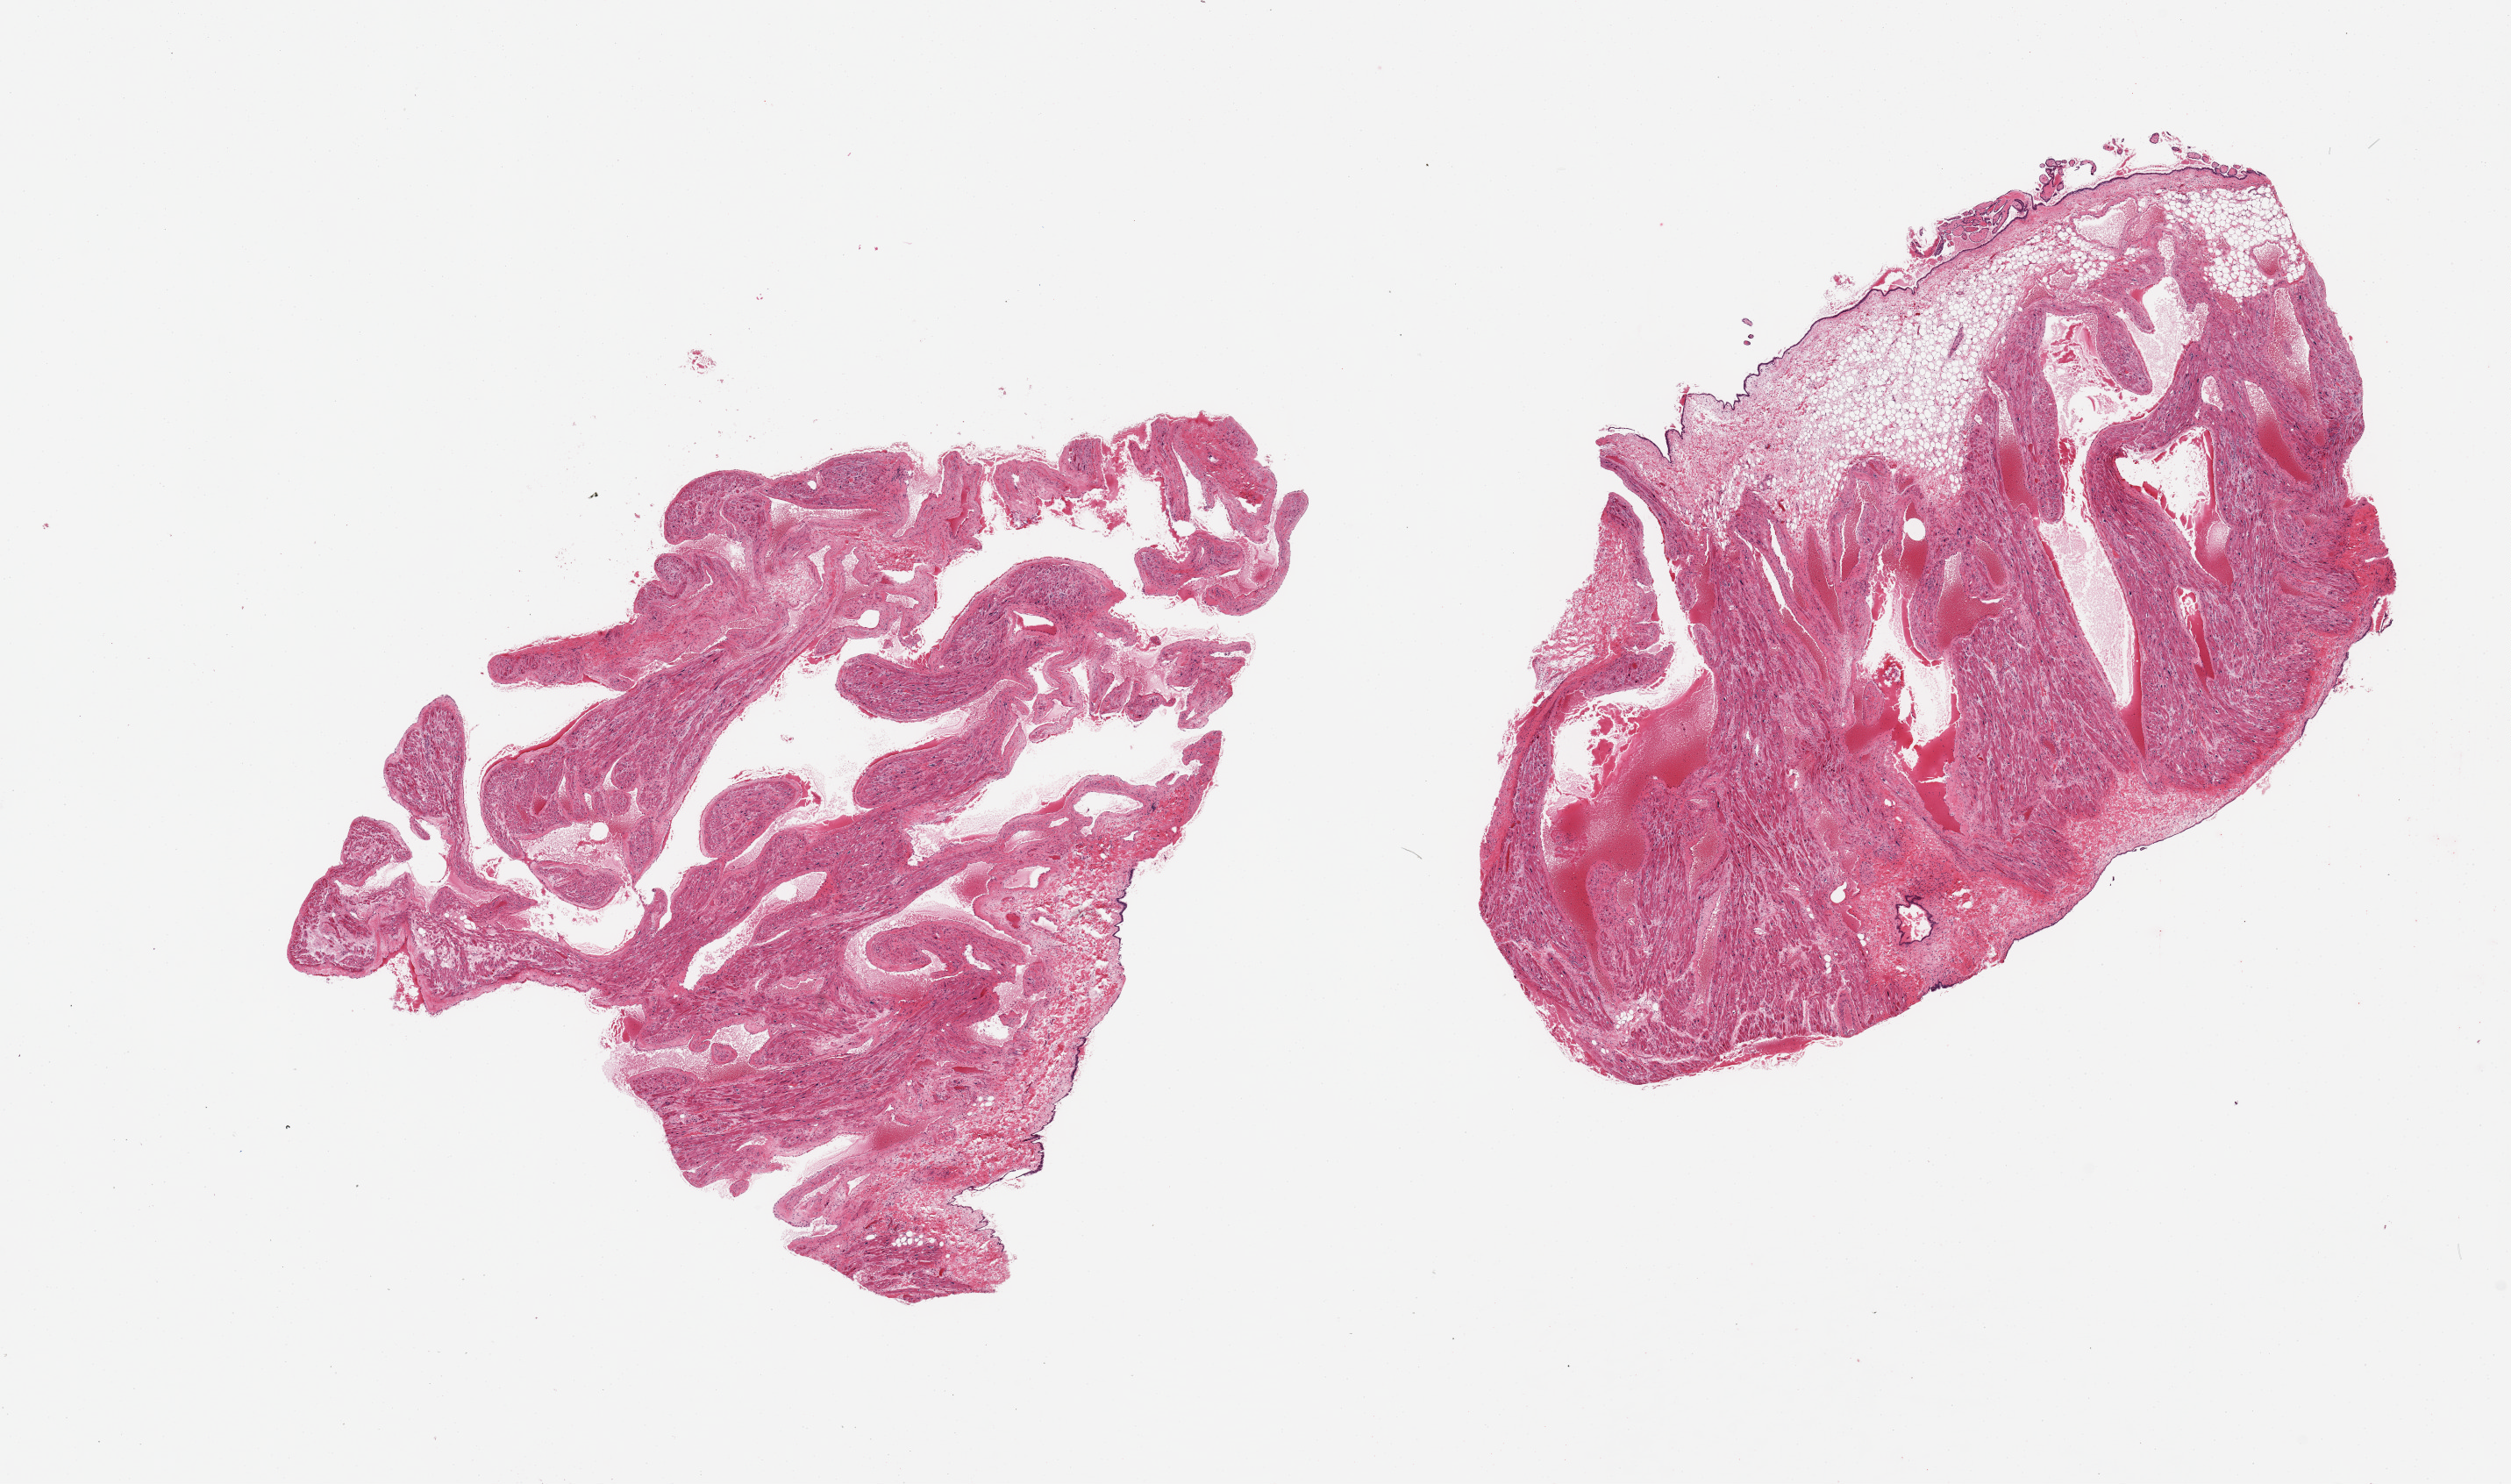
Whole-slide image, H&E stain — whole scanned area (about 22.6 x 13.4 mm, from a 20x scan) shown as a low-resolution overview, PAXgene-fixed, paraffin-embedded tissue, target tissue: auricular appendage, donor tissue sample. Donor sex: female.
Review note (as recorded): 2 pieces; 30% internal fibrofatty content.